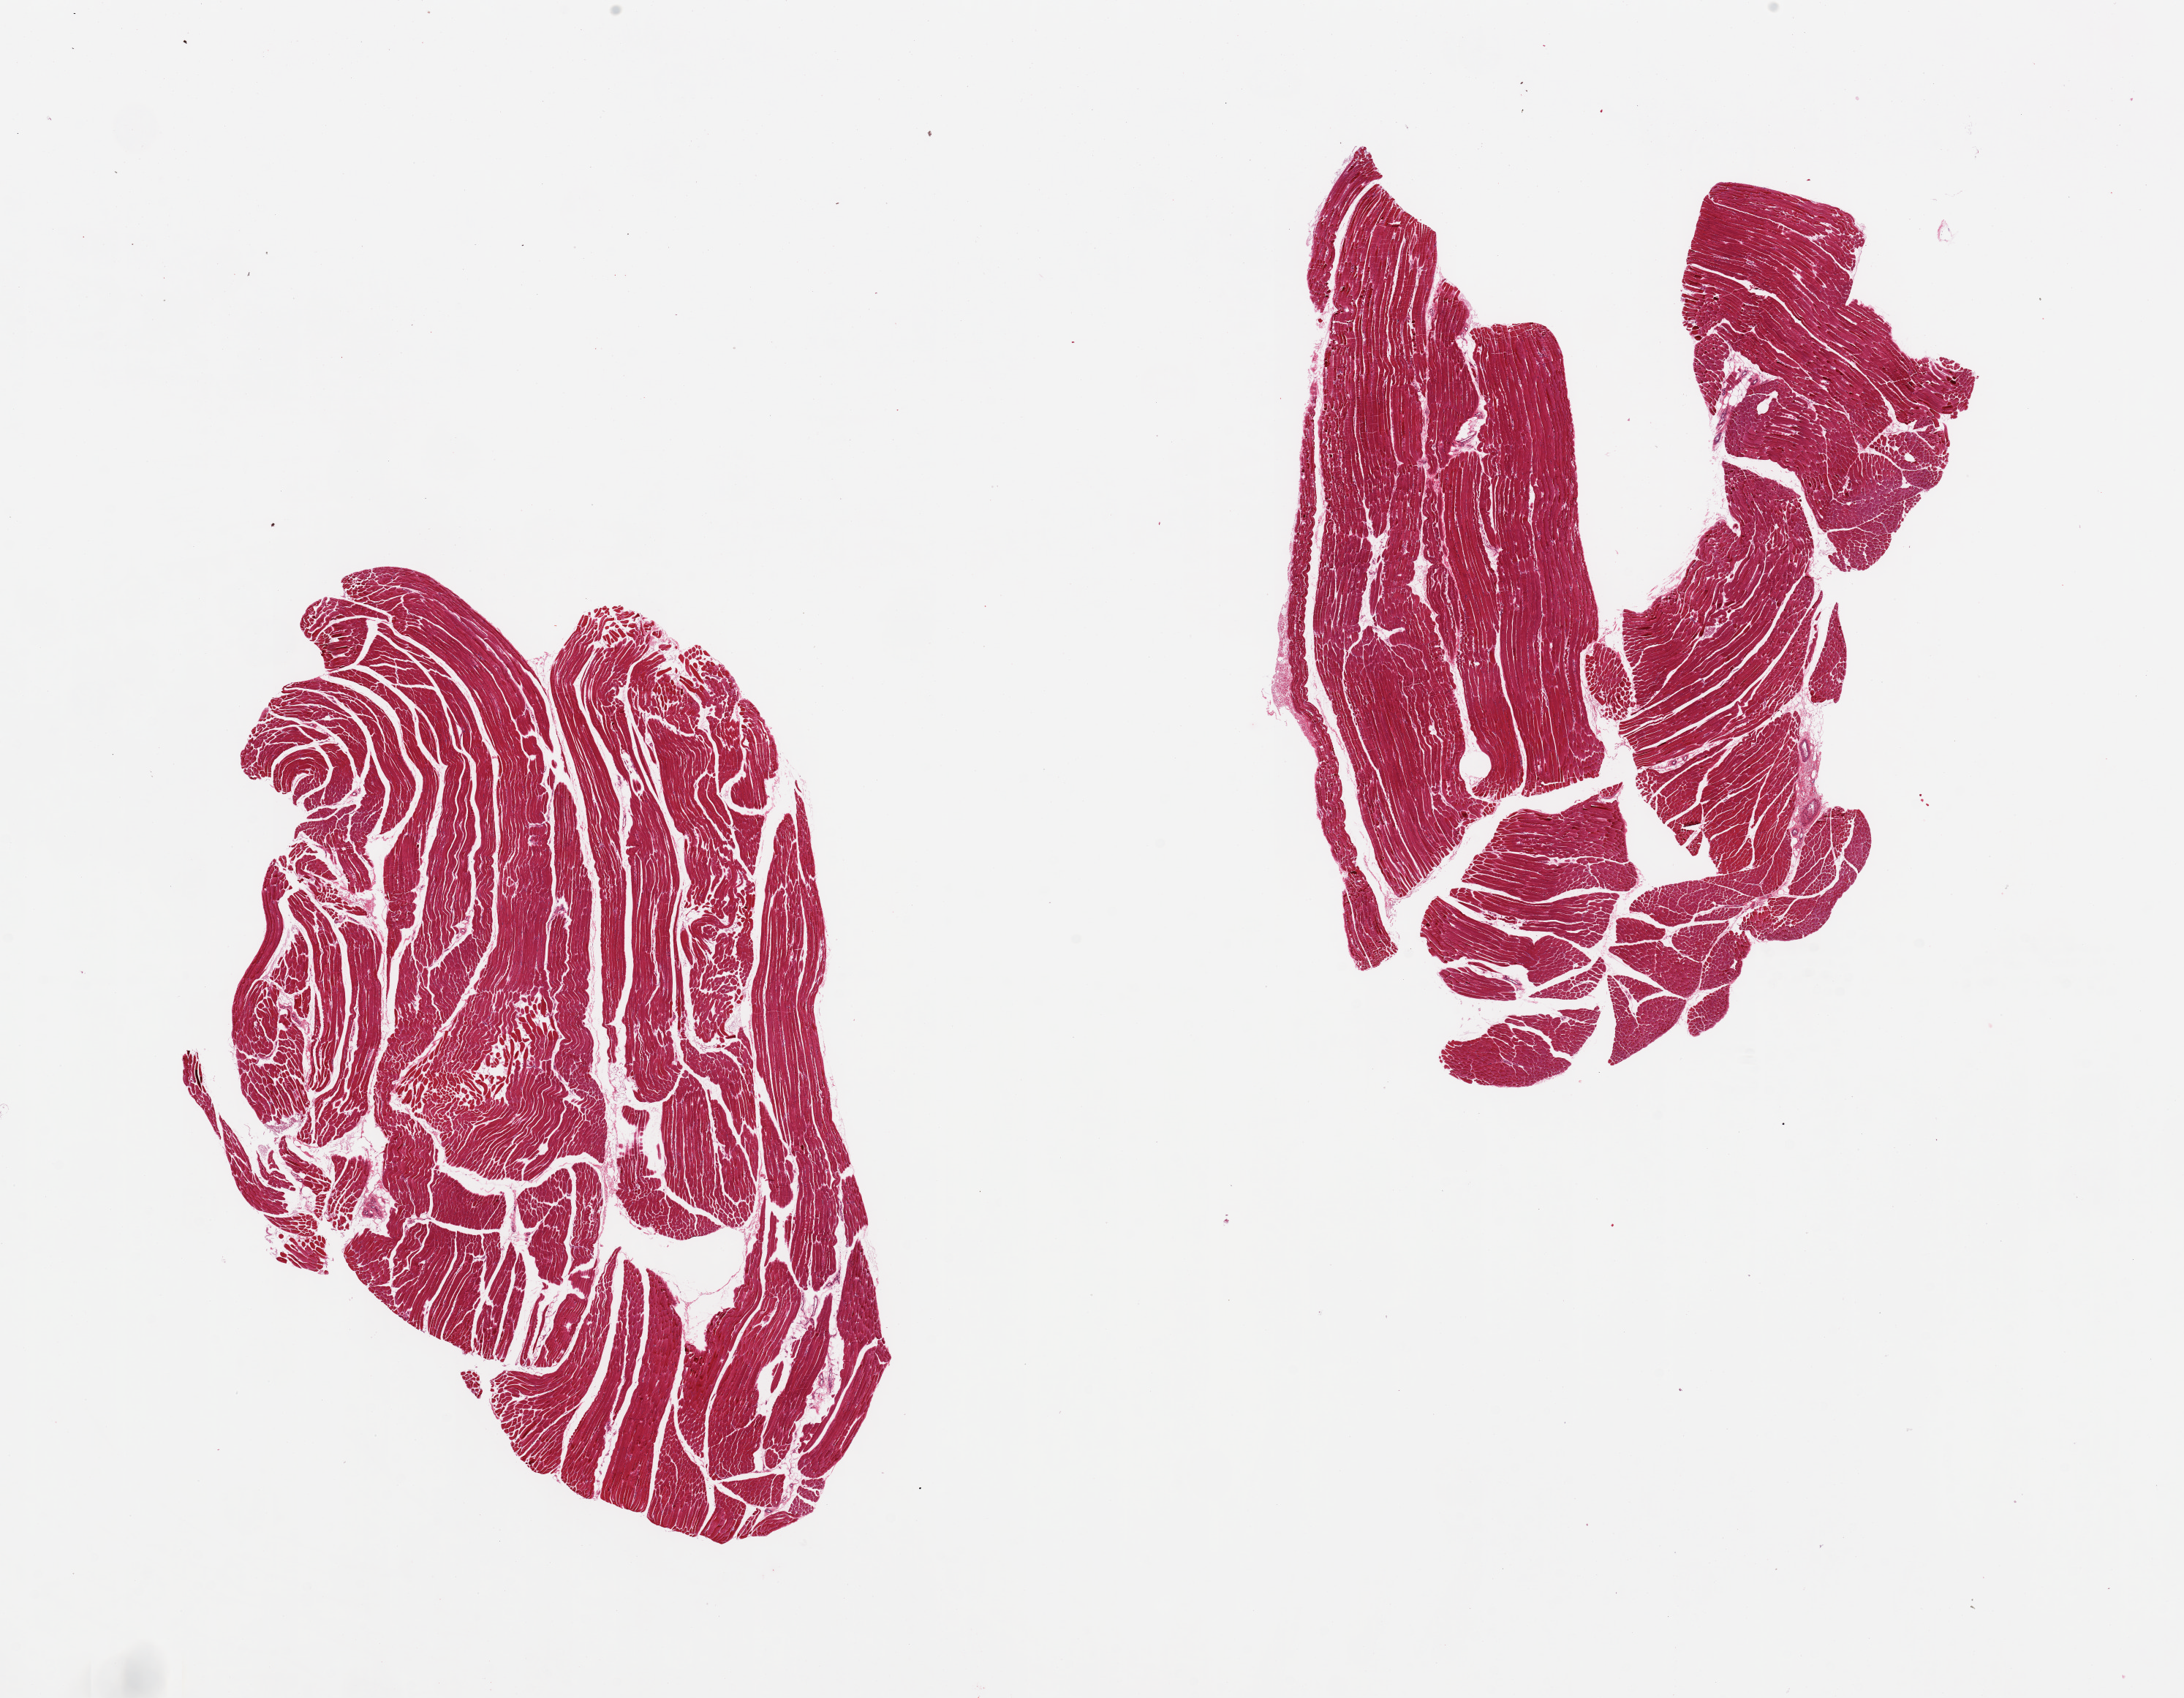
Haematoxylin and eosin whole-slide image, a low-resolution overview of the entire scanned area, about 23.6 x 18.4 mm. PAXgene-fixed, paraffin-embedded tissue. Sampled site (target tissue): skeletal muscle. Tissue donor sample. Donor sex: female.
Pathologist's review note for this sample: 2 pieces.